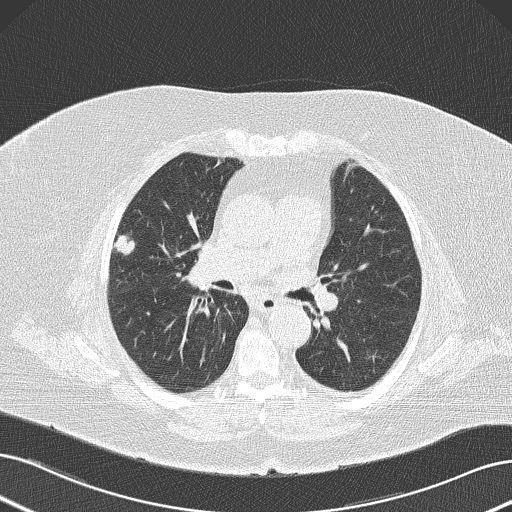
Low-dose screening chest CT, one axial slice. Slice 78 of 145 in the series (ordered by position). Reconstruction kernel B50f. Lung window (W 1500 / L -600 HU). 2 mm slice thickness. 512 × 512 image matrix.
Structures marked on this image (manually delineated by an expert):
- lesion 1 (tumor, upper lobe of right lung): bounding box <114,235,135,256> (left, top, right, bottom; pixels)